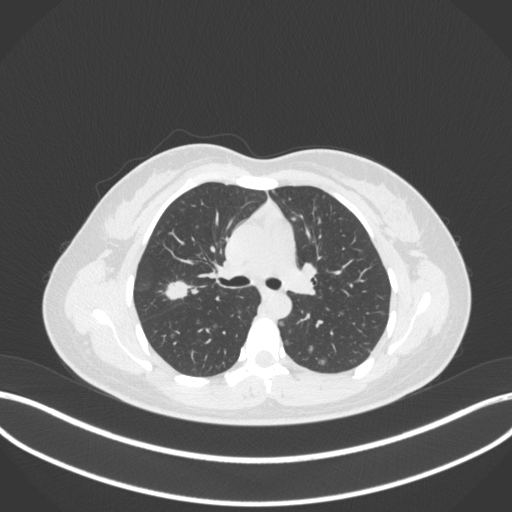
Chest CT, one axial slice. Slice 213 of 214 in the series (ordered by position). Reconstruction kernel B31f. 120 kVp. Lung window (W 1500 / L -600 HU). 1 mm slice thickness. 512 × 512 image matrix. Patient: female, 33 years. Case-level facts recorded for this patient, not image findings: clinical TNM (as recorded): T1c N0 M0; histopathological grade: G2-G3.
Annotated regions visible in this slice (bounding box drawn by a radiologist):
- lung tumour (recorded histology: adenocarcinoma): bounding box (x1, y1, x2, y2) in pixels: (163, 278, 191, 303)